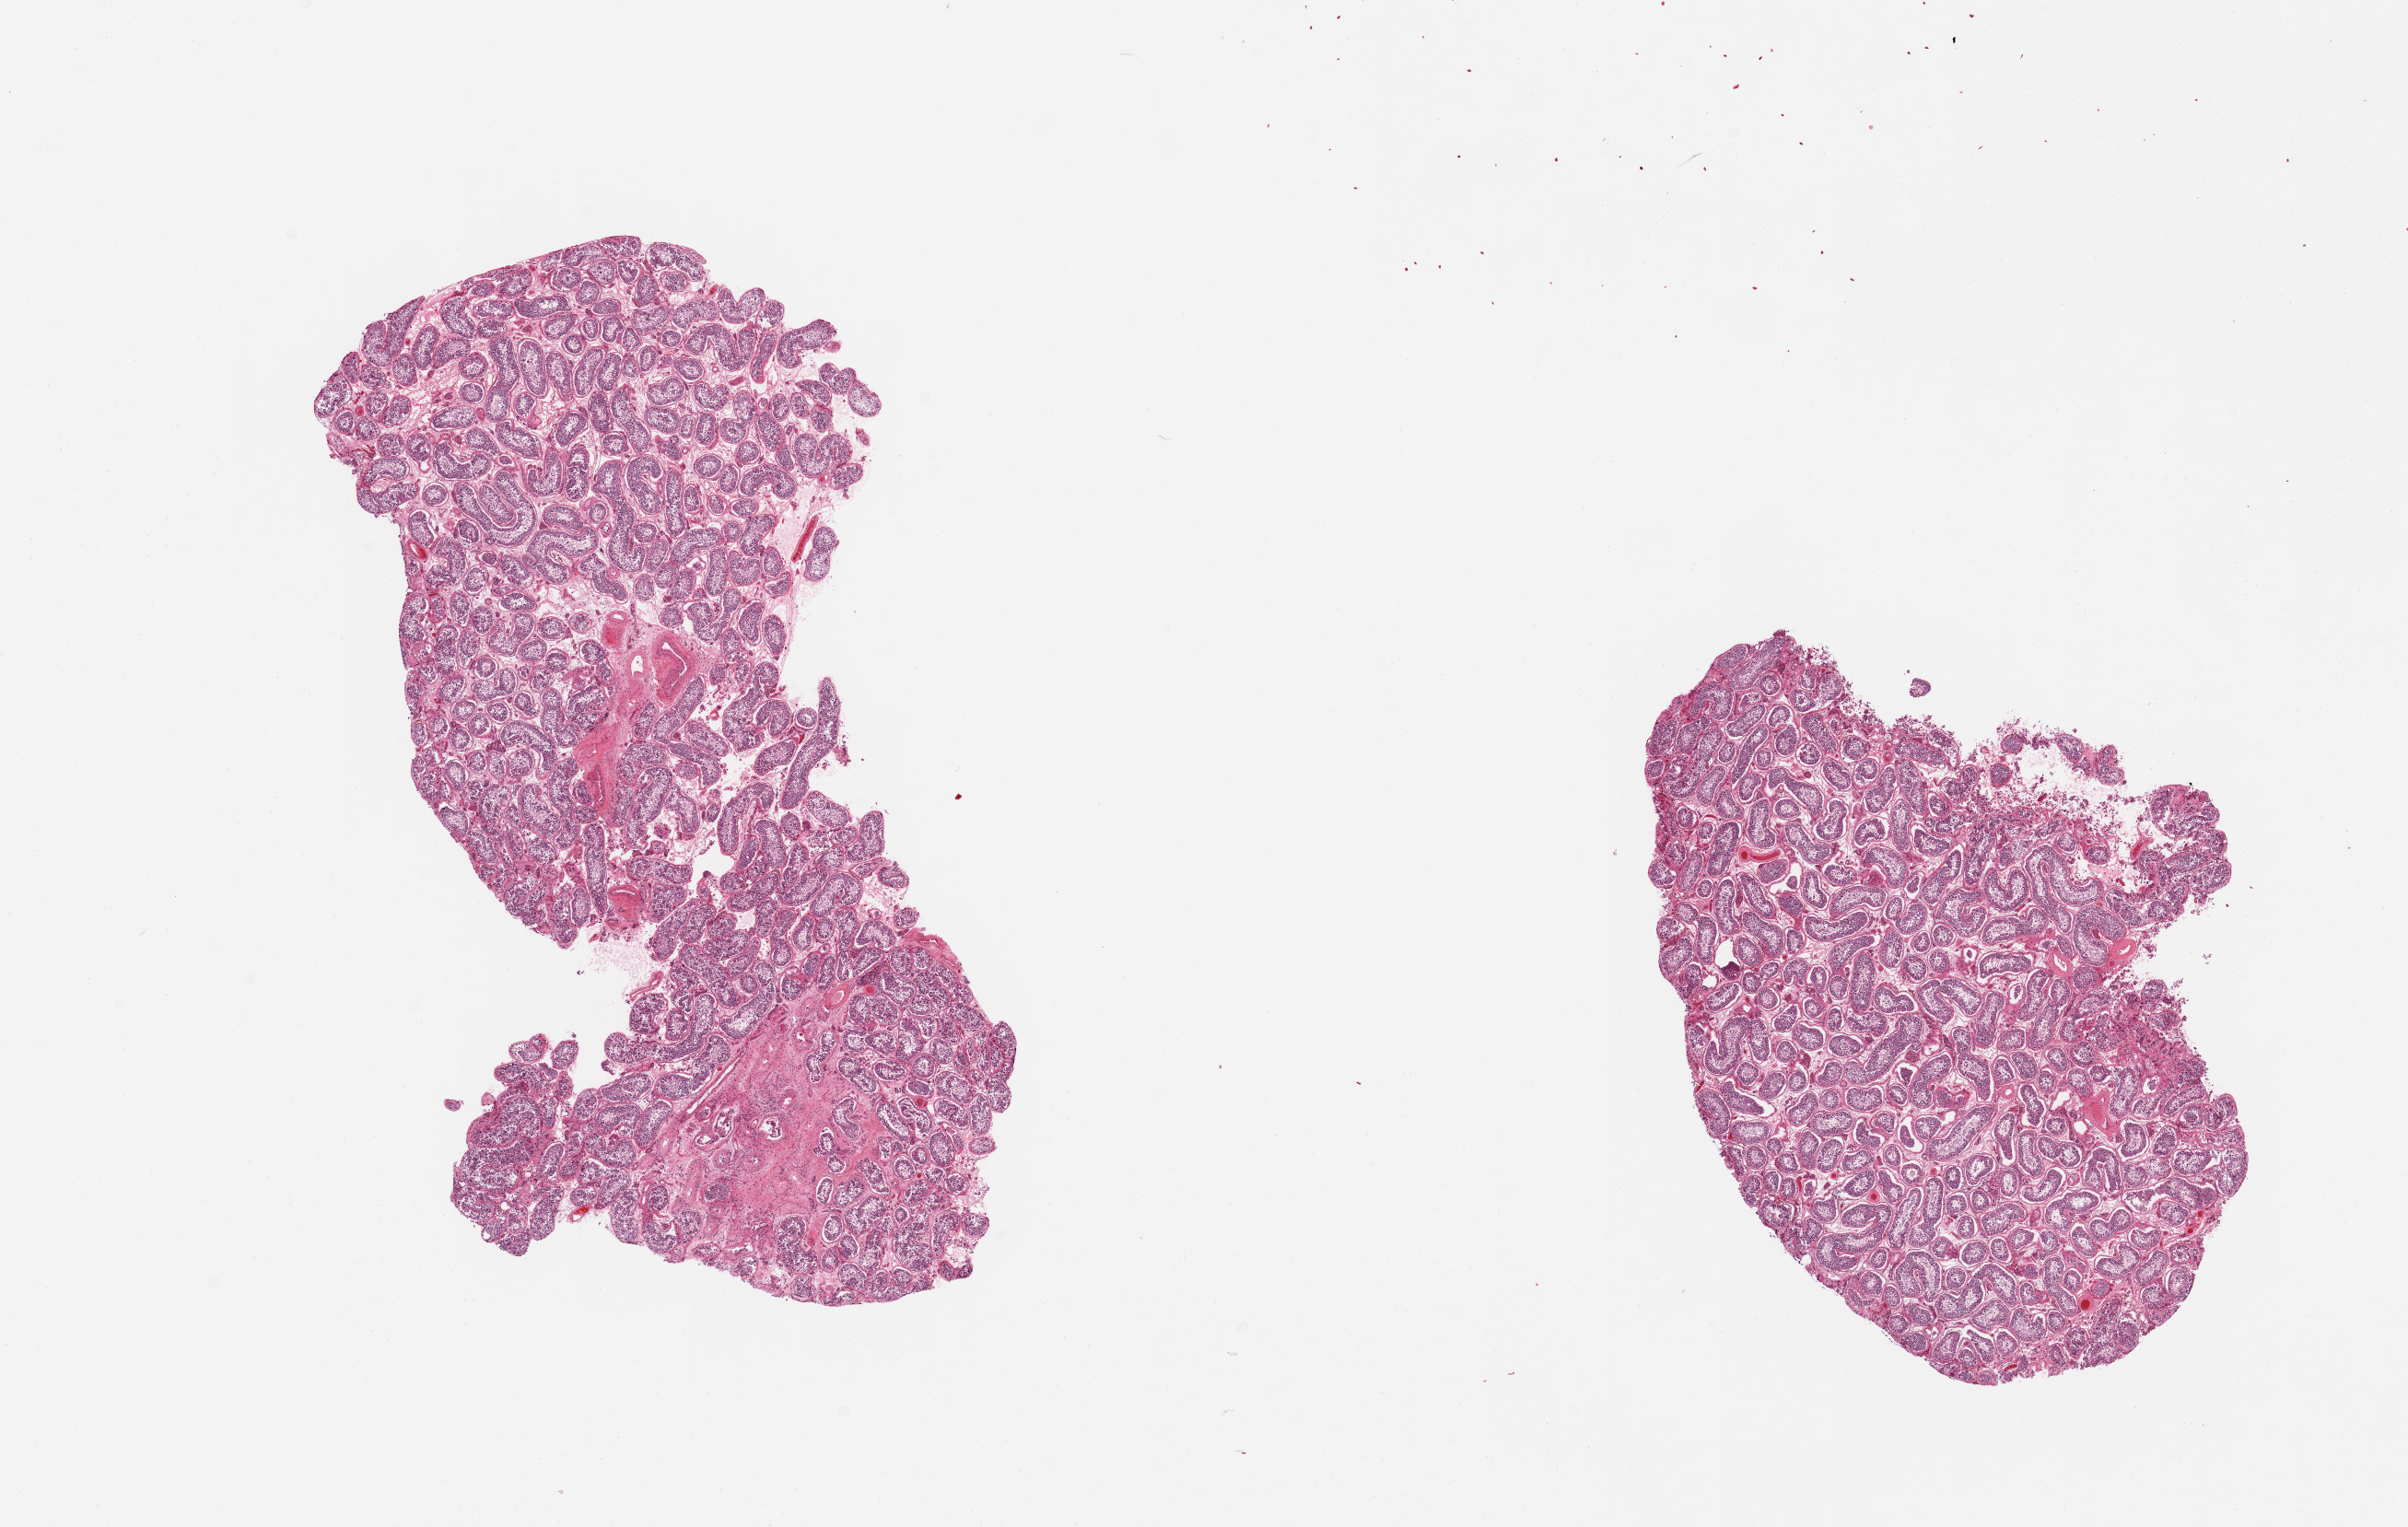
Whole-slide image, hematoxylin and eosin (H&E) stain, shown as a low-resolution overview of the whole scanned area (about 20.7 x 13.1 mm); PAXgene-fixed, paraffin-embedded tissue; sampled site (target tissue): testis; donor tissue sample.
Reviewer comment on this tissue sample: 2 pieces, active spermatogenesis, arteriosclerosis.